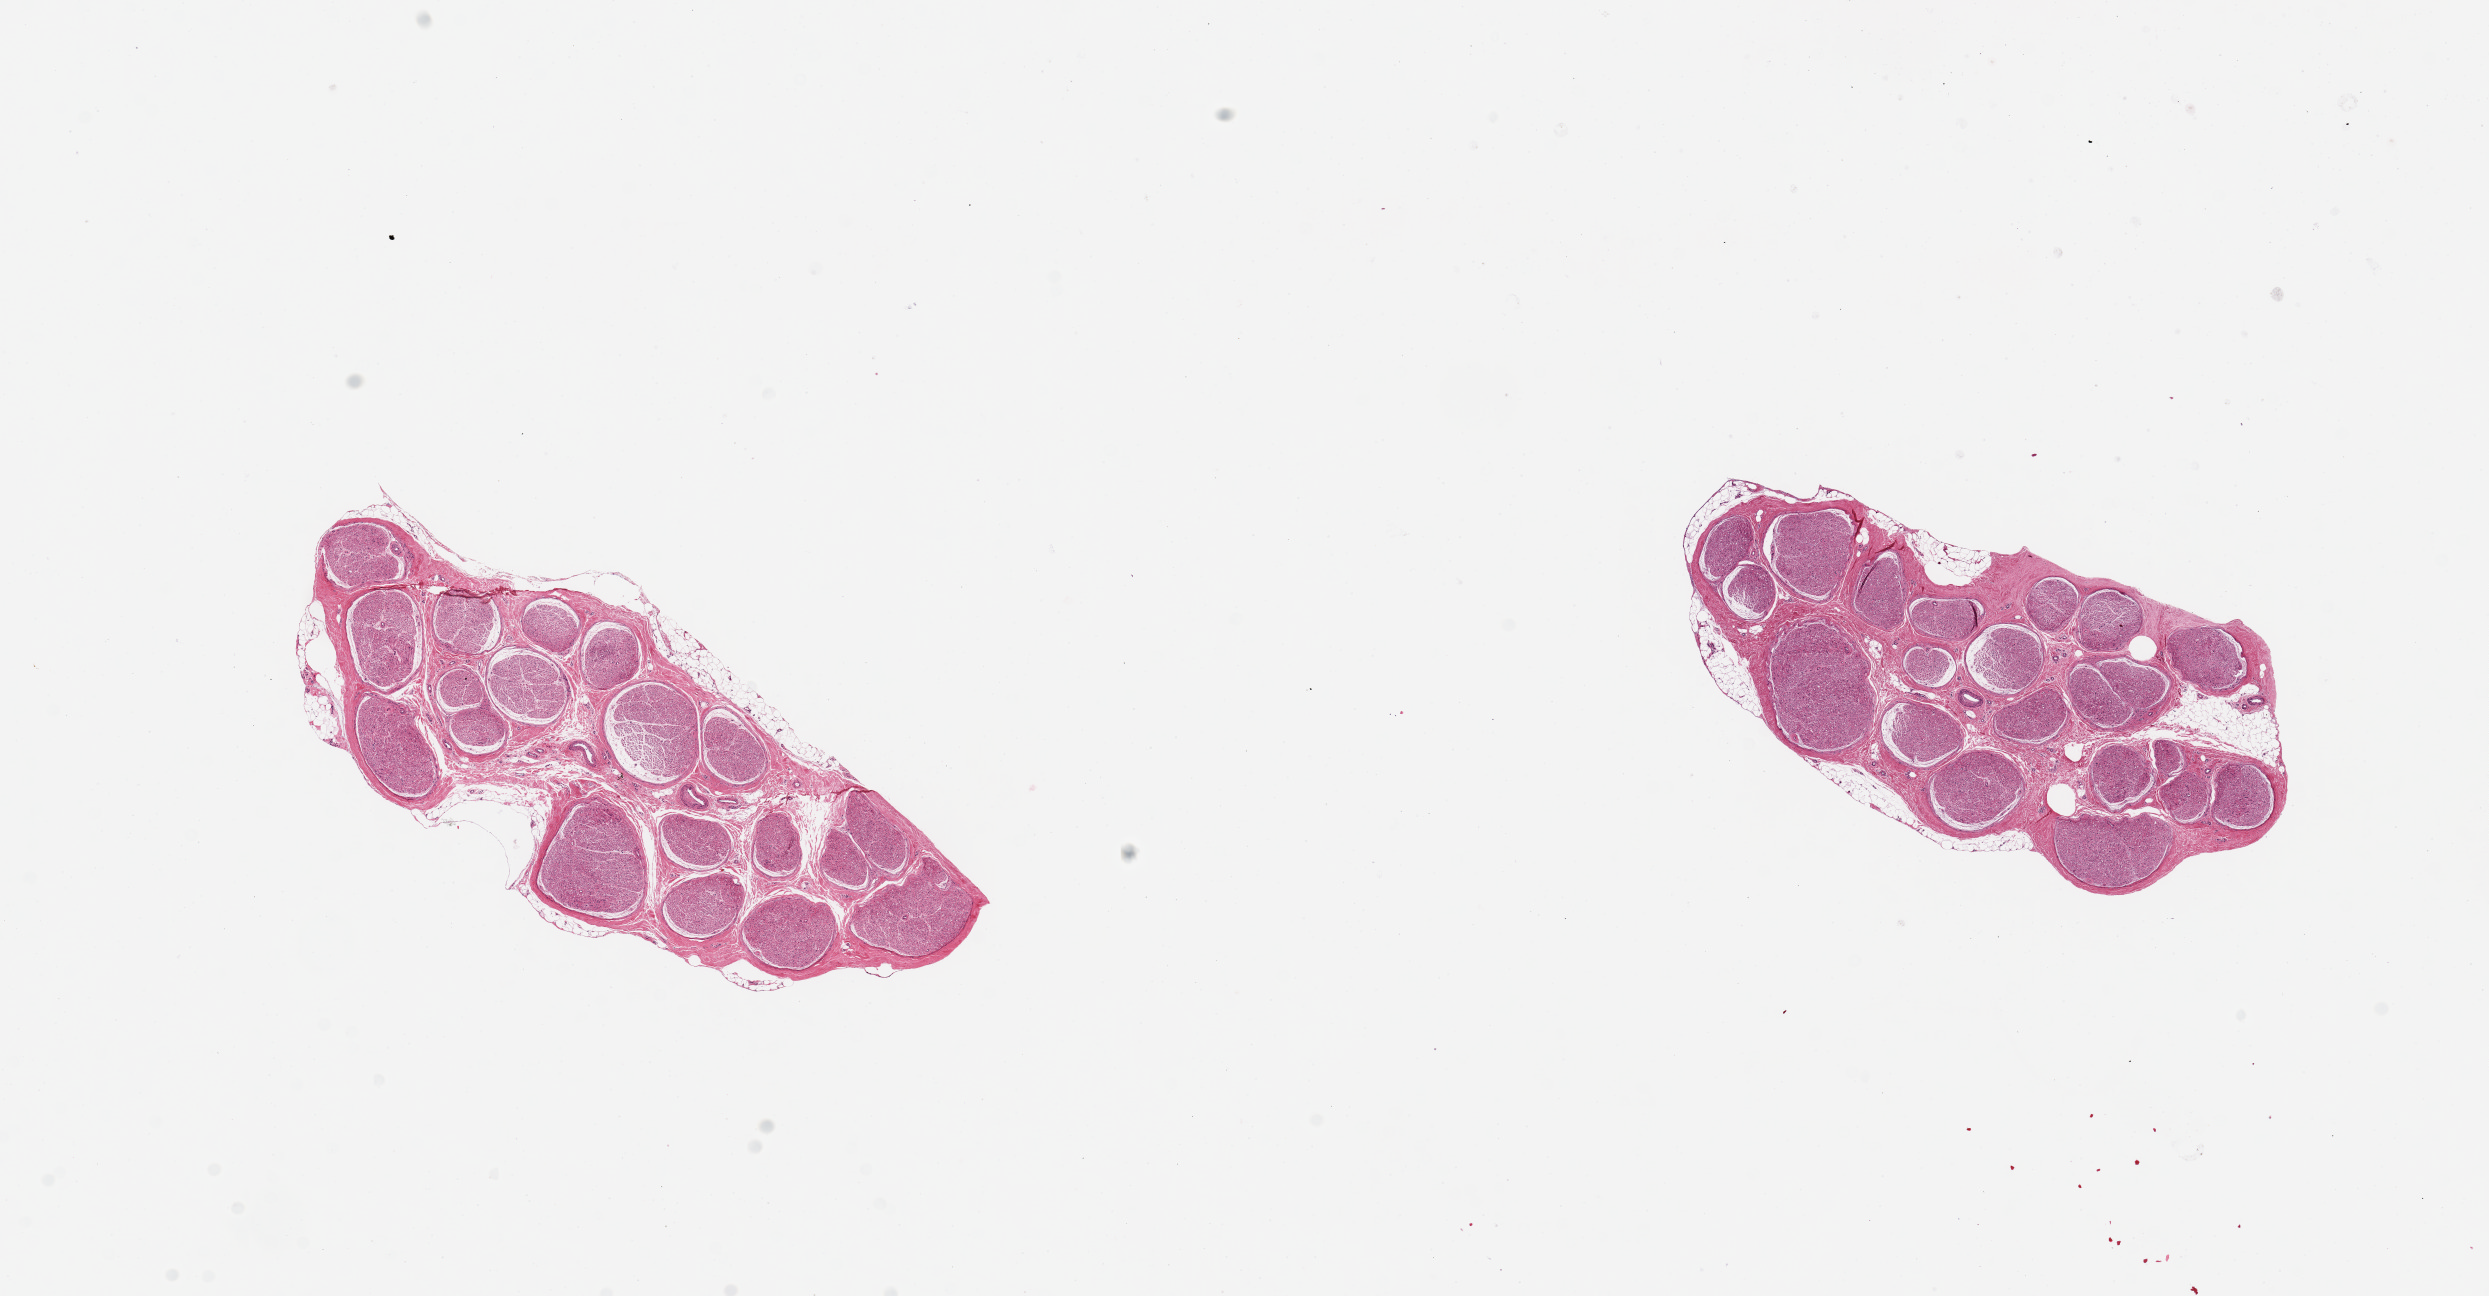
H&E whole-slide image, brightfield — shown as a low-resolution overview of the whole scanned area (about 19.7 x 10.3 mm). PAXgene-fixed paraffin-embedded (PFPE) section. Section of tibial nerve (target tissue). Donor tissue sample. Donor sex: male.
Pathologist's review note for this sample: 2 pieces, 6x2.5 & 5x3mm; good clean specimen, minimal (<0.1mm) adherent fat on one aliquot.